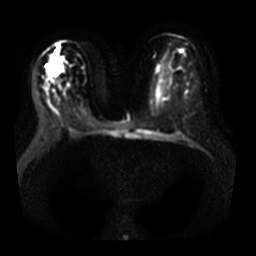
Breast MRI, one axial slice; diffusion-weighted series; image 2 of 4 stored at this slice position (different b-values; order by instance number); 3 T; 5 mm slice thickness; 256 × 256 image matrix, field of view 350 × 350 mm. Female patient.
Outlined on this slice (outlined manually by an expert reader):
- tumour on diffusion-weighted imaging: box from (x=47, y=70) to (x=50, y=72) px